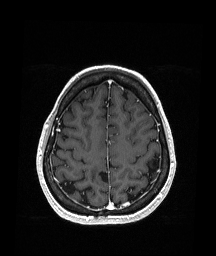
Brain MRI from a brain-tumour surgery series, one axial slice; position 57 of 151 along the scan axis; T1-weighted post-contrast; 216 × 256 image matrix, field of view 211 × 250 mm. Case-level facts recorded for this patient, not image findings: histopathology: Oligodendroglioma; WHO grade: 2; IDH mutation: yes; tumour location: Right Parietal.
Structures marked on this image (manually delineated by an expert):
- previous resection cavity: bounding box [x1, y1, x2, y2] px = [94, 168, 109, 180]